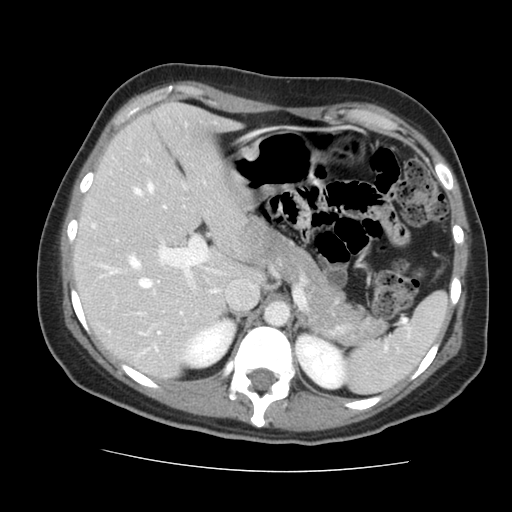
Contrast-enhanced abdominal CT, one axial slice. Slice 97 of 144 in the series (ordered by position). 120 kVp. Intravenous contrast given. Soft-tissue window (W 400 / L 40 HU). 512 × 512 image matrix, field of view 333 × 333 mm. Female patient, age 46 years. Case-level facts recorded for this patient, not image findings: diagnosis: colorectal cancer liver metastases, imaged before liver resection; multiple liver metastases: no; largest metastasis: 2.8 cm; chemotherapy before resection: yes.
Outlined on this slice (outlined manually by an expert reader):
- hepatic veins: bounding box (x1, y1, x2, y2) in pixels: (134, 184, 216, 292)
- liver: (75, 104, 258, 376)
- planned liver remnant (the part of the liver to remain after resection): (75, 104, 258, 376)
- portal vein (with intrahepatic branches): (110, 236, 210, 350)